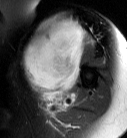
MRI of an extremity soft-tissue mass, one axial slice; position 51 of 87 along the scan axis; T2-weighted fat-saturated; MR volume resampled by the dataset authors to the PET/CT grid (not the native acquisition matrix); 127 × 138 image matrix. Female patient. From the clinical record (not read from this slice): histological type: pleiomorphic leiomyosarcoma; grade: high; site of the primary tumour: left biceps.
Outlined on this slice (expert contour drawn on MRI and transferred to this co-registered scan by the dataset authors):
- gross tumour volume including surrounding oedema: box from (x=22, y=16) to (x=89, y=108) px
- gross tumour volume (mass): (x=22, y=18)–(x=85, y=97)